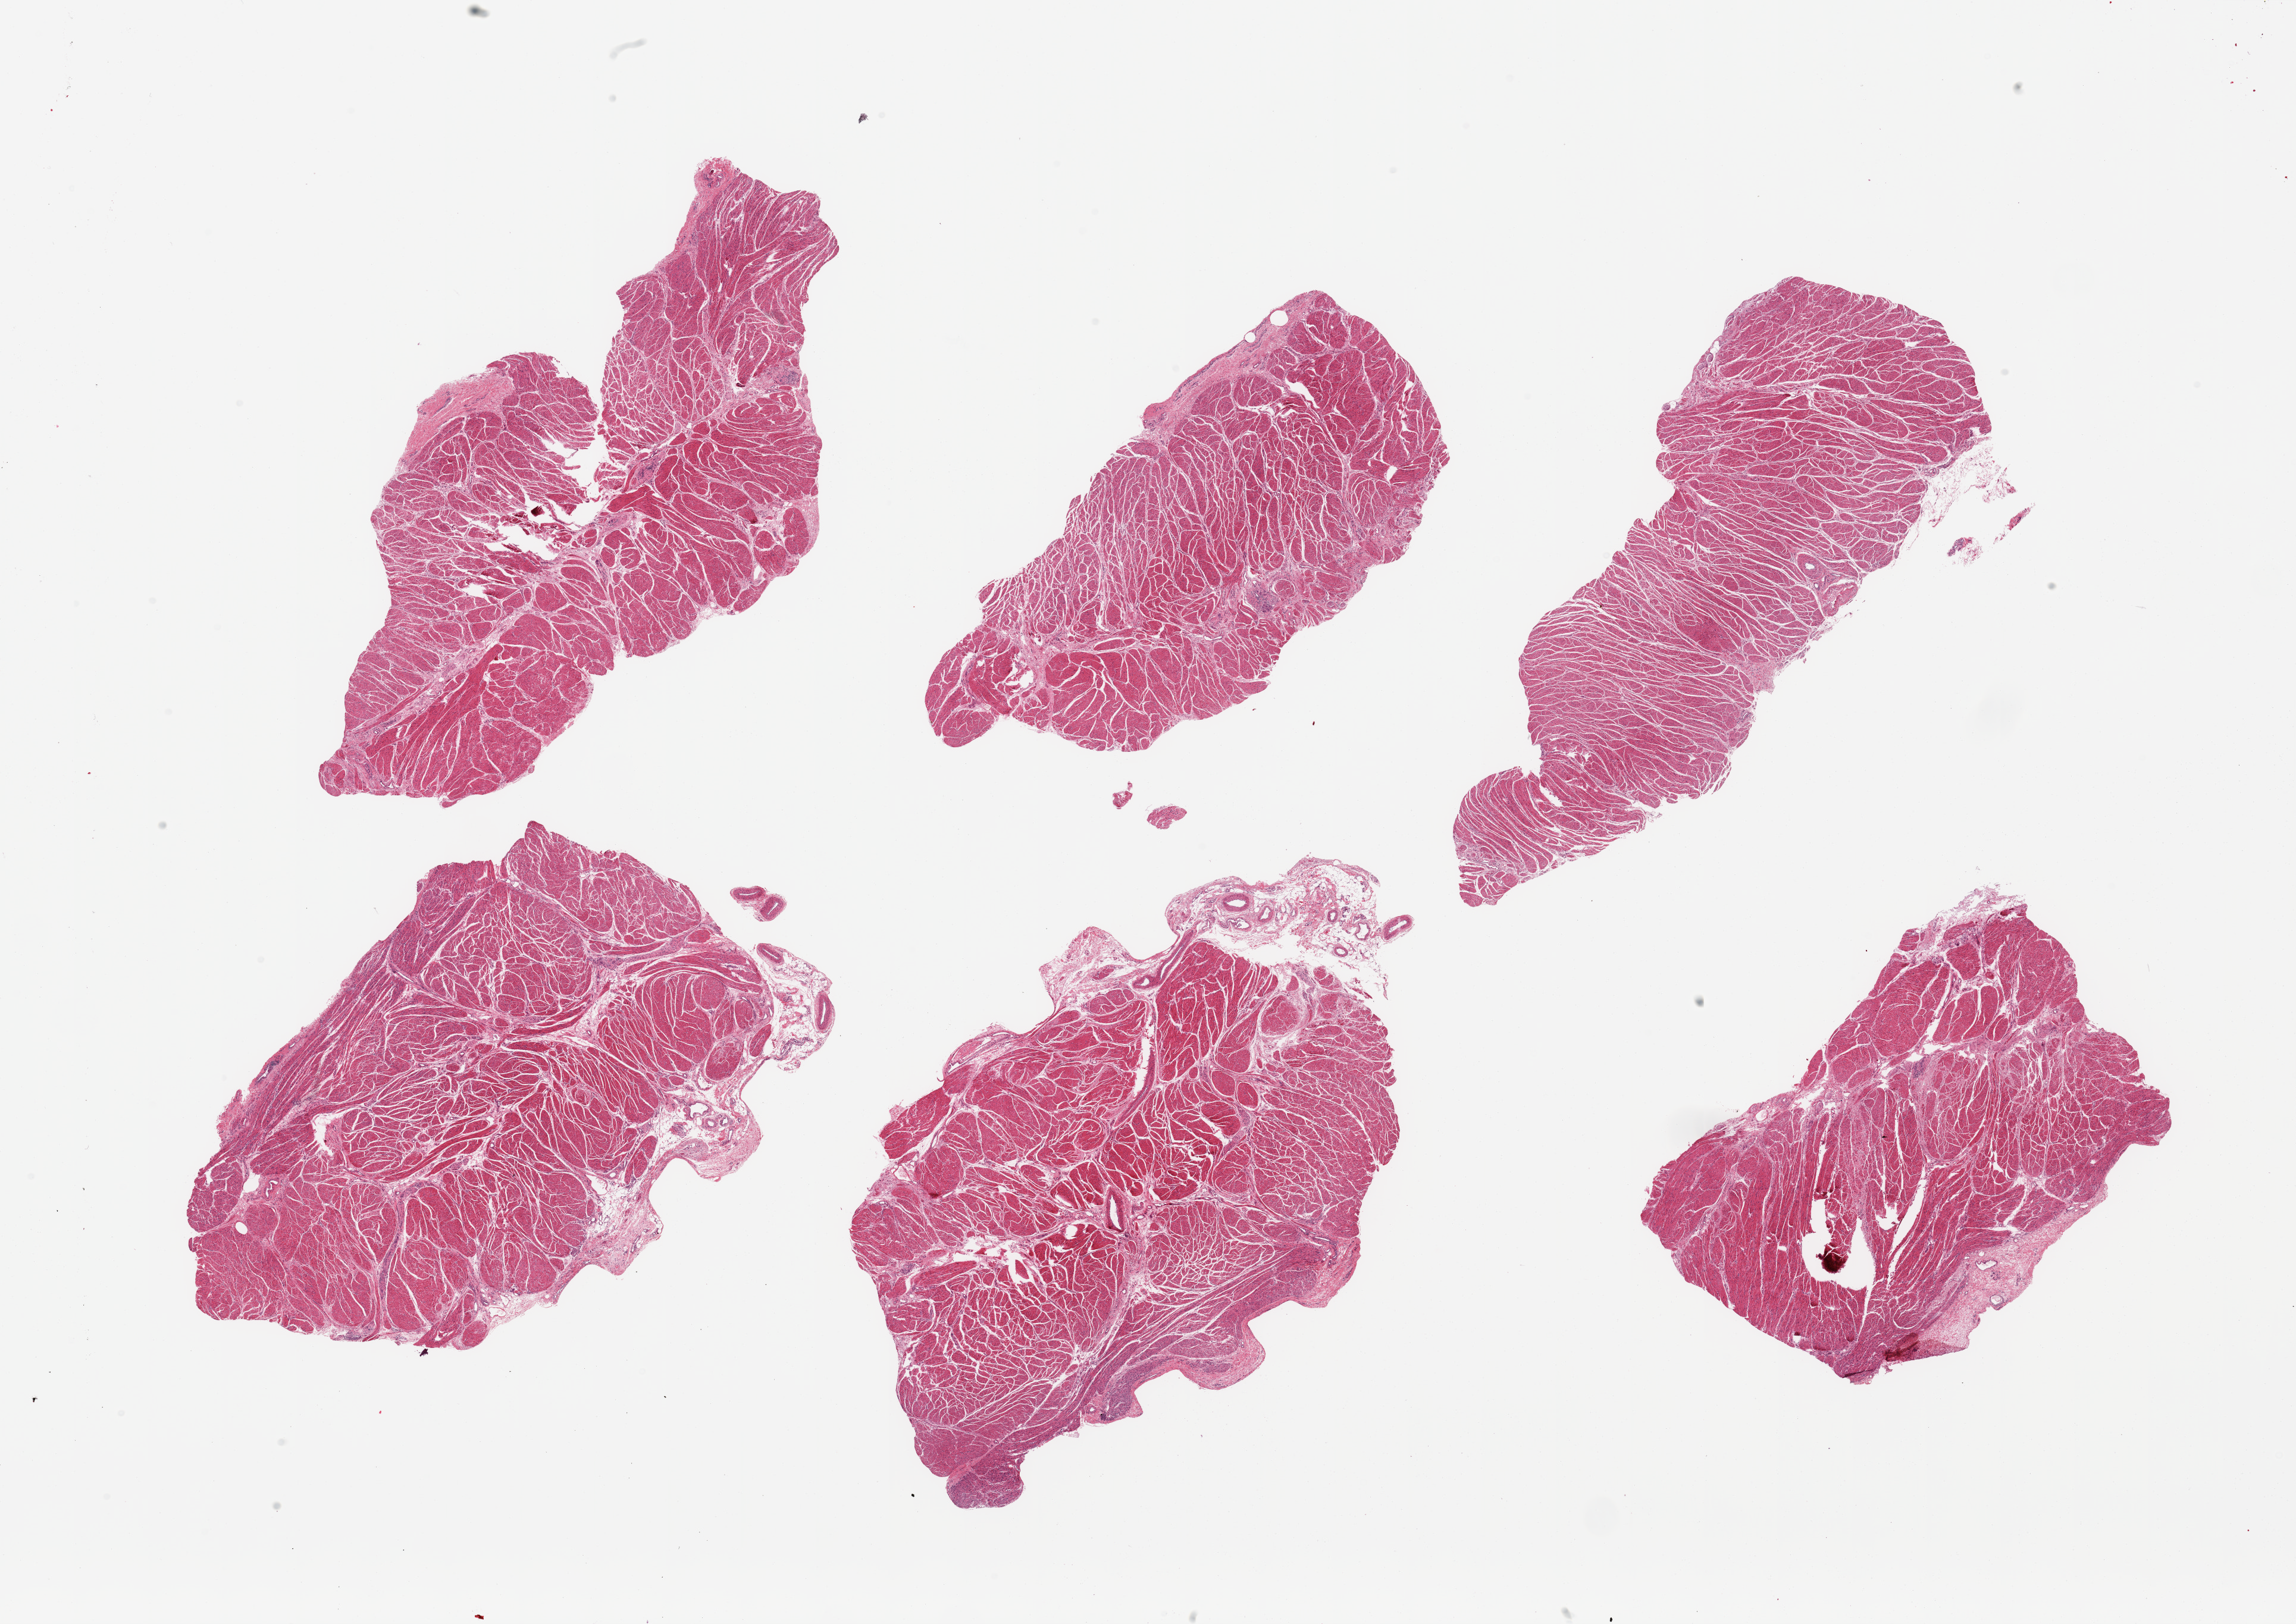
Whole-slide image, hematoxylin and eosin (H&E) stain, whole scanned area (about 30.5 x 21.6 mm, from a 20x scan) shown as a low-resolution overview, PAXgene-fixed, paraffin-embedded tissue, sampled site (target tissue): gastroesophageal junction, tissue donor sample. Donor: male.
Reviewer comment on this tissue sample: 6 pieces; well dissected.